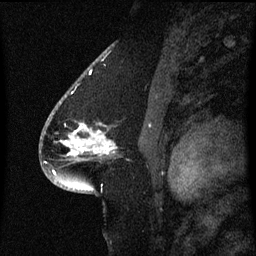
Breast MRI (dynamic contrast-enhanced), one sagittal slice. Position 39 of 60 along the scan axis. Dynamic contrast-enhanced series, image 2 of 3 at this slice position (ordered by acquisition). 1.5 T. TE 4.2 ms, TR 8.4 ms. 256 × 256 image matrix, field of view 200 × 200 mm. Female patient, age 54 years. From the clinical record (not read from this slice): setting: breast cancer imaged before/during neoadjuvant chemotherapy; receptor status: HR-positive, HER2-negative.
Structures marked on this image (semi-automatic segmentation, software-assisted and operator-edited):
- analysis volume of interest (the breast-tissue region the enhancement analysis was run in; not a lesion): bounding box [x1, y1, x2, y2] px = [48, 102, 117, 161]
- tumour enhancement mask (voxels above the 70 % enhancement threshold inside the analysis volume of interest): [65, 126, 111, 155]